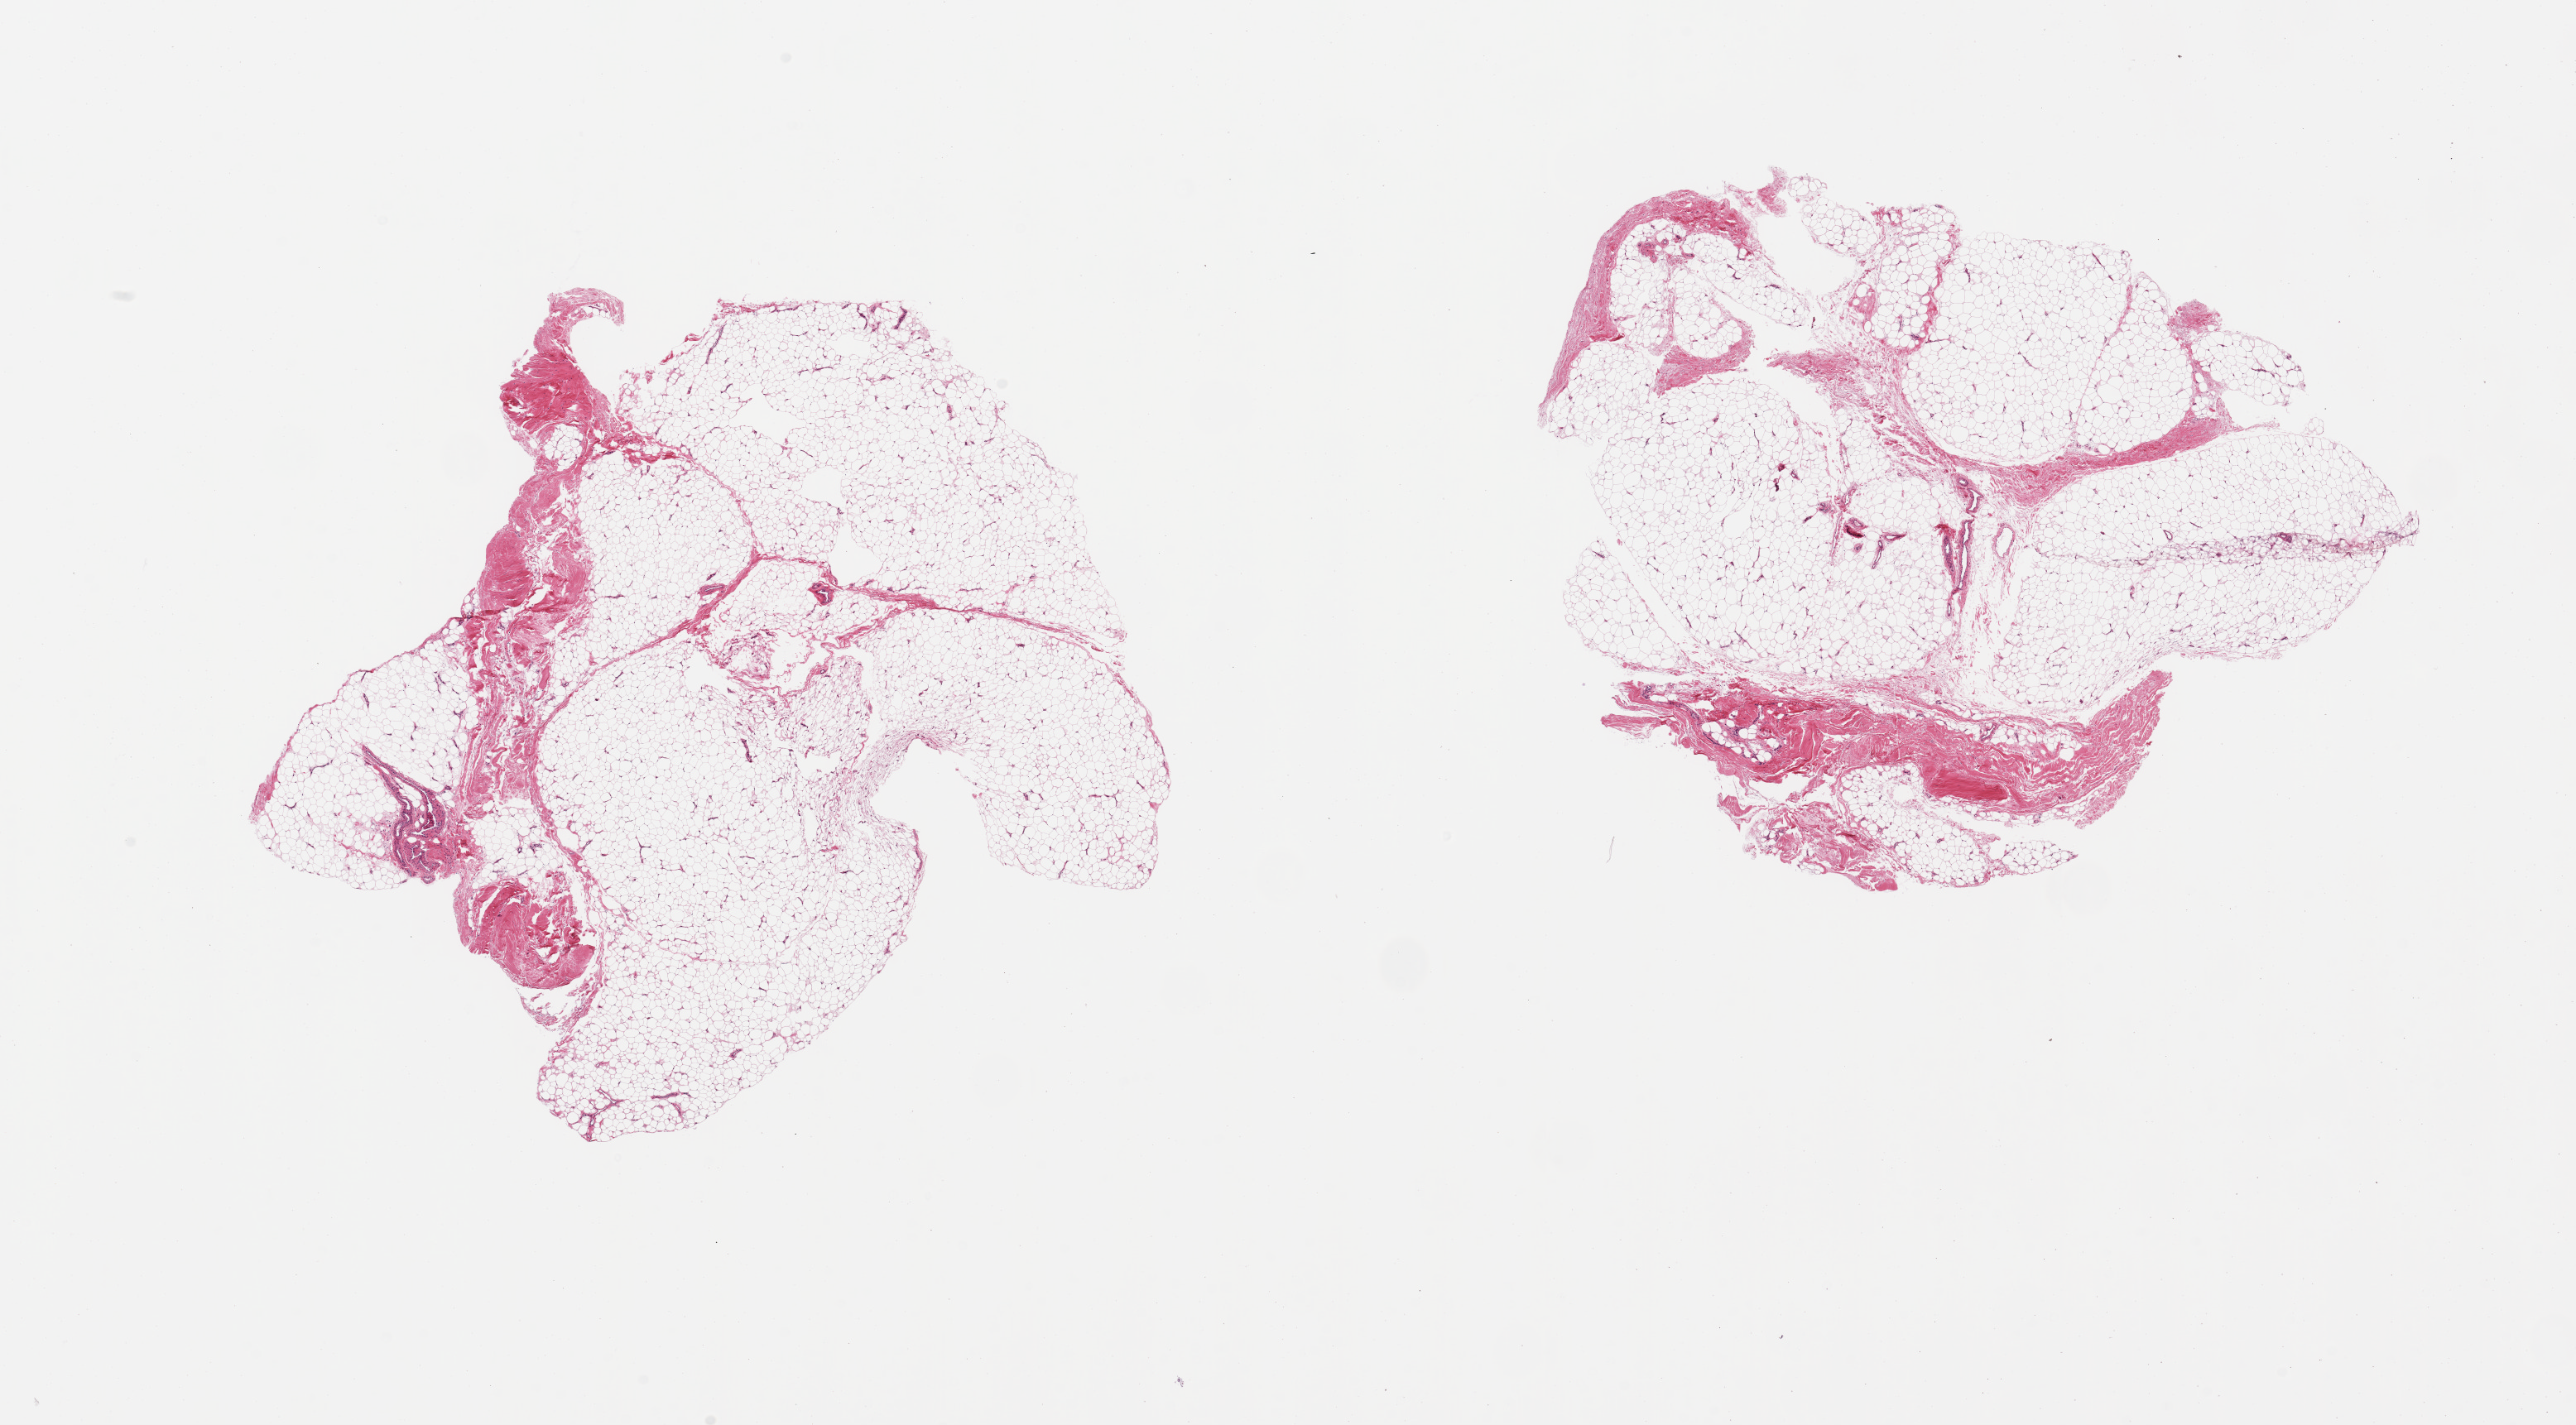
Whole-slide image, haematoxylin and eosin stain, brightfield — whole scanned area (about 24.6 x 13.6 mm, acquisition: 20x scan) shown as a low-resolution overview, PAXgene-fixed paraffin-embedded (PFPE) section, section of adipose tissue (target tissue), donor tissue sample.
Pathologist's review note for this sample: 2 pieces; mature adipose tissue and ~15% fibrovascular component.